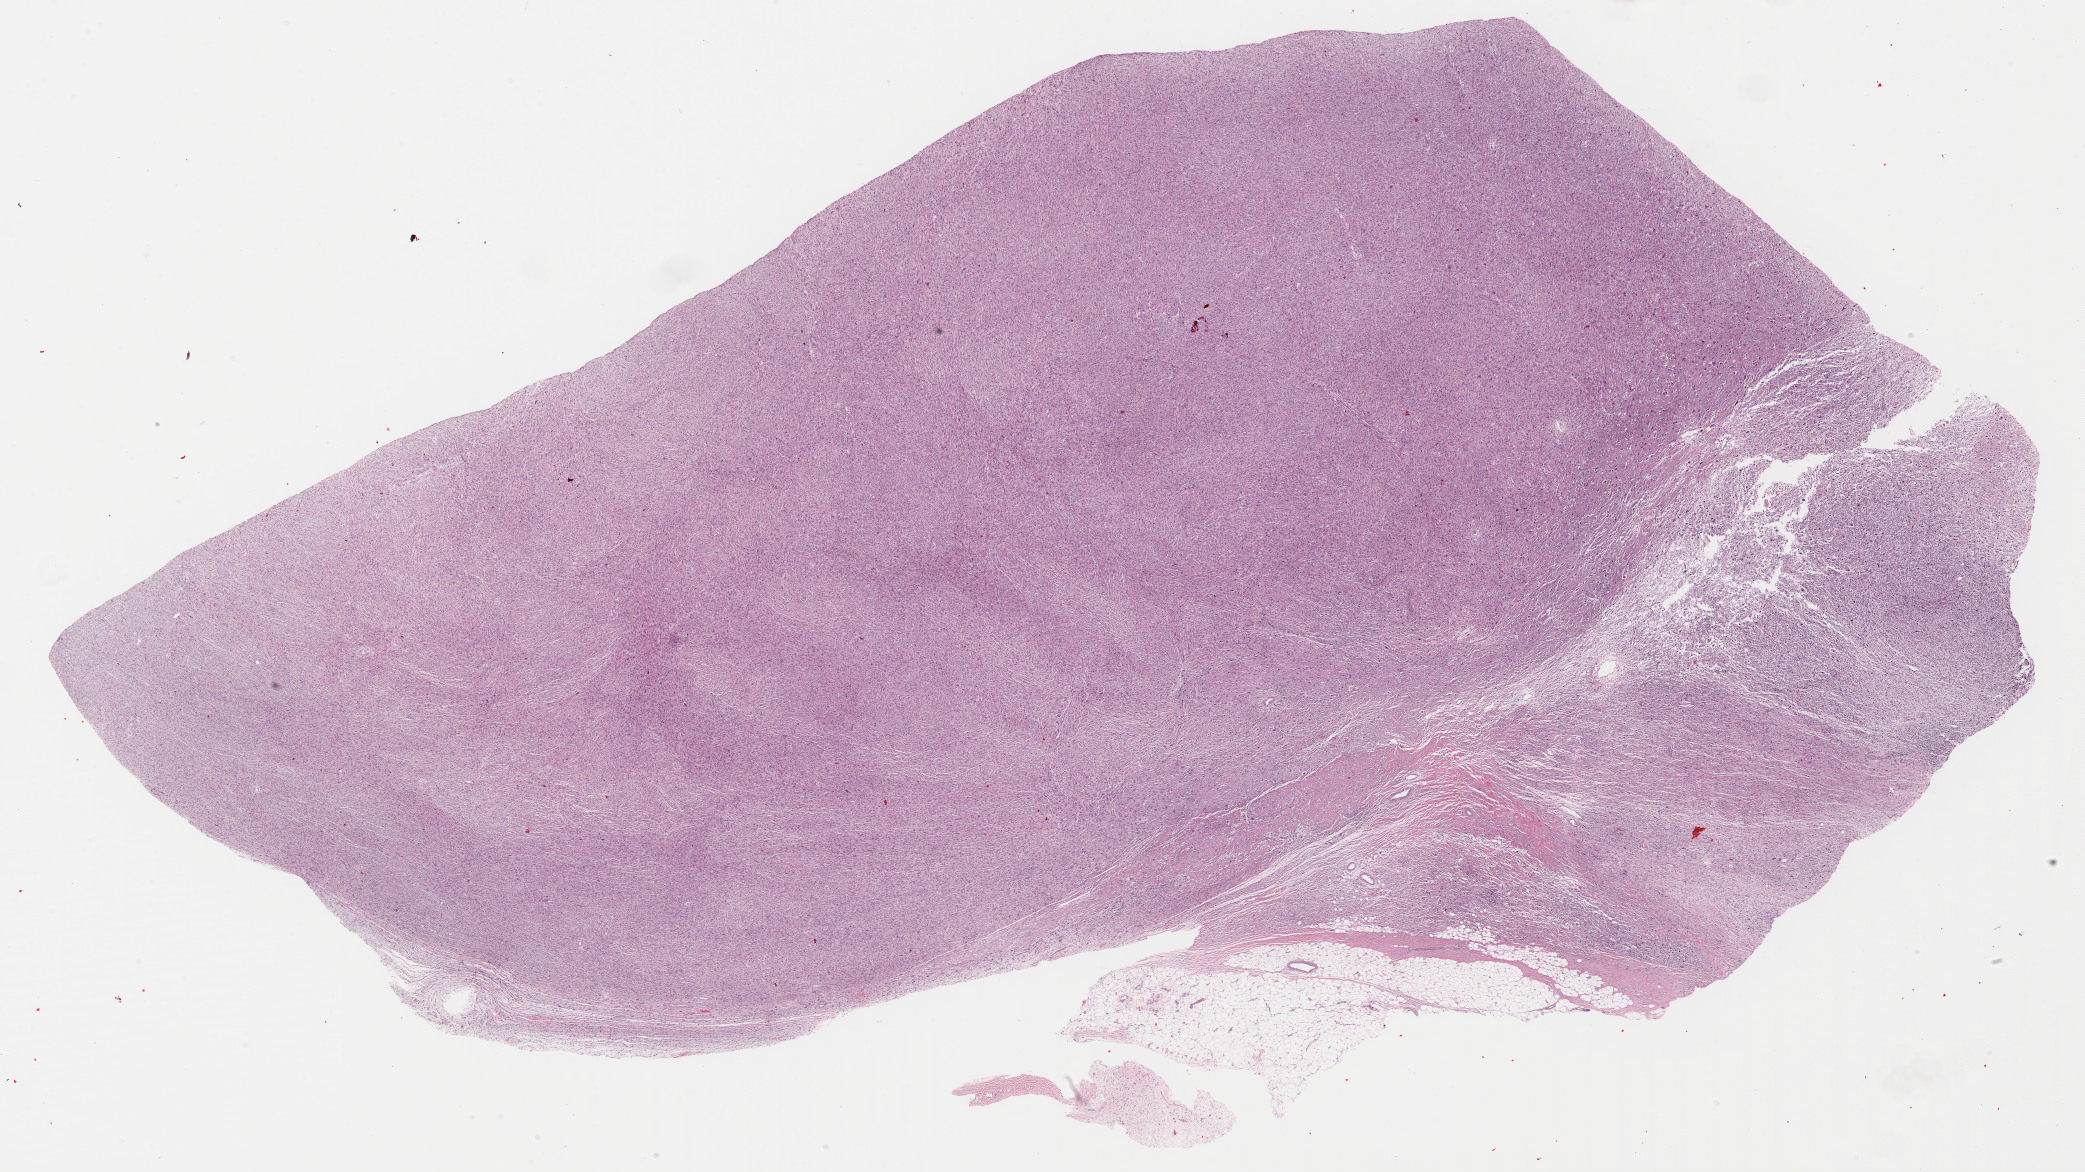
Hematoxylin and eosin (H&E) stained whole-slide image, whole scanned area (about 33.7 x 19.0 mm) shown as a low-resolution overview. Formalin-fixed paraffin-embedded (FFPE) diagnostic section. Primary tumour sample from the retroperitoneum and peritoneum. Patient: male, age at initial diagnosis 79 years.
* pathologic diagnosis: Dedifferentiated liposarcoma